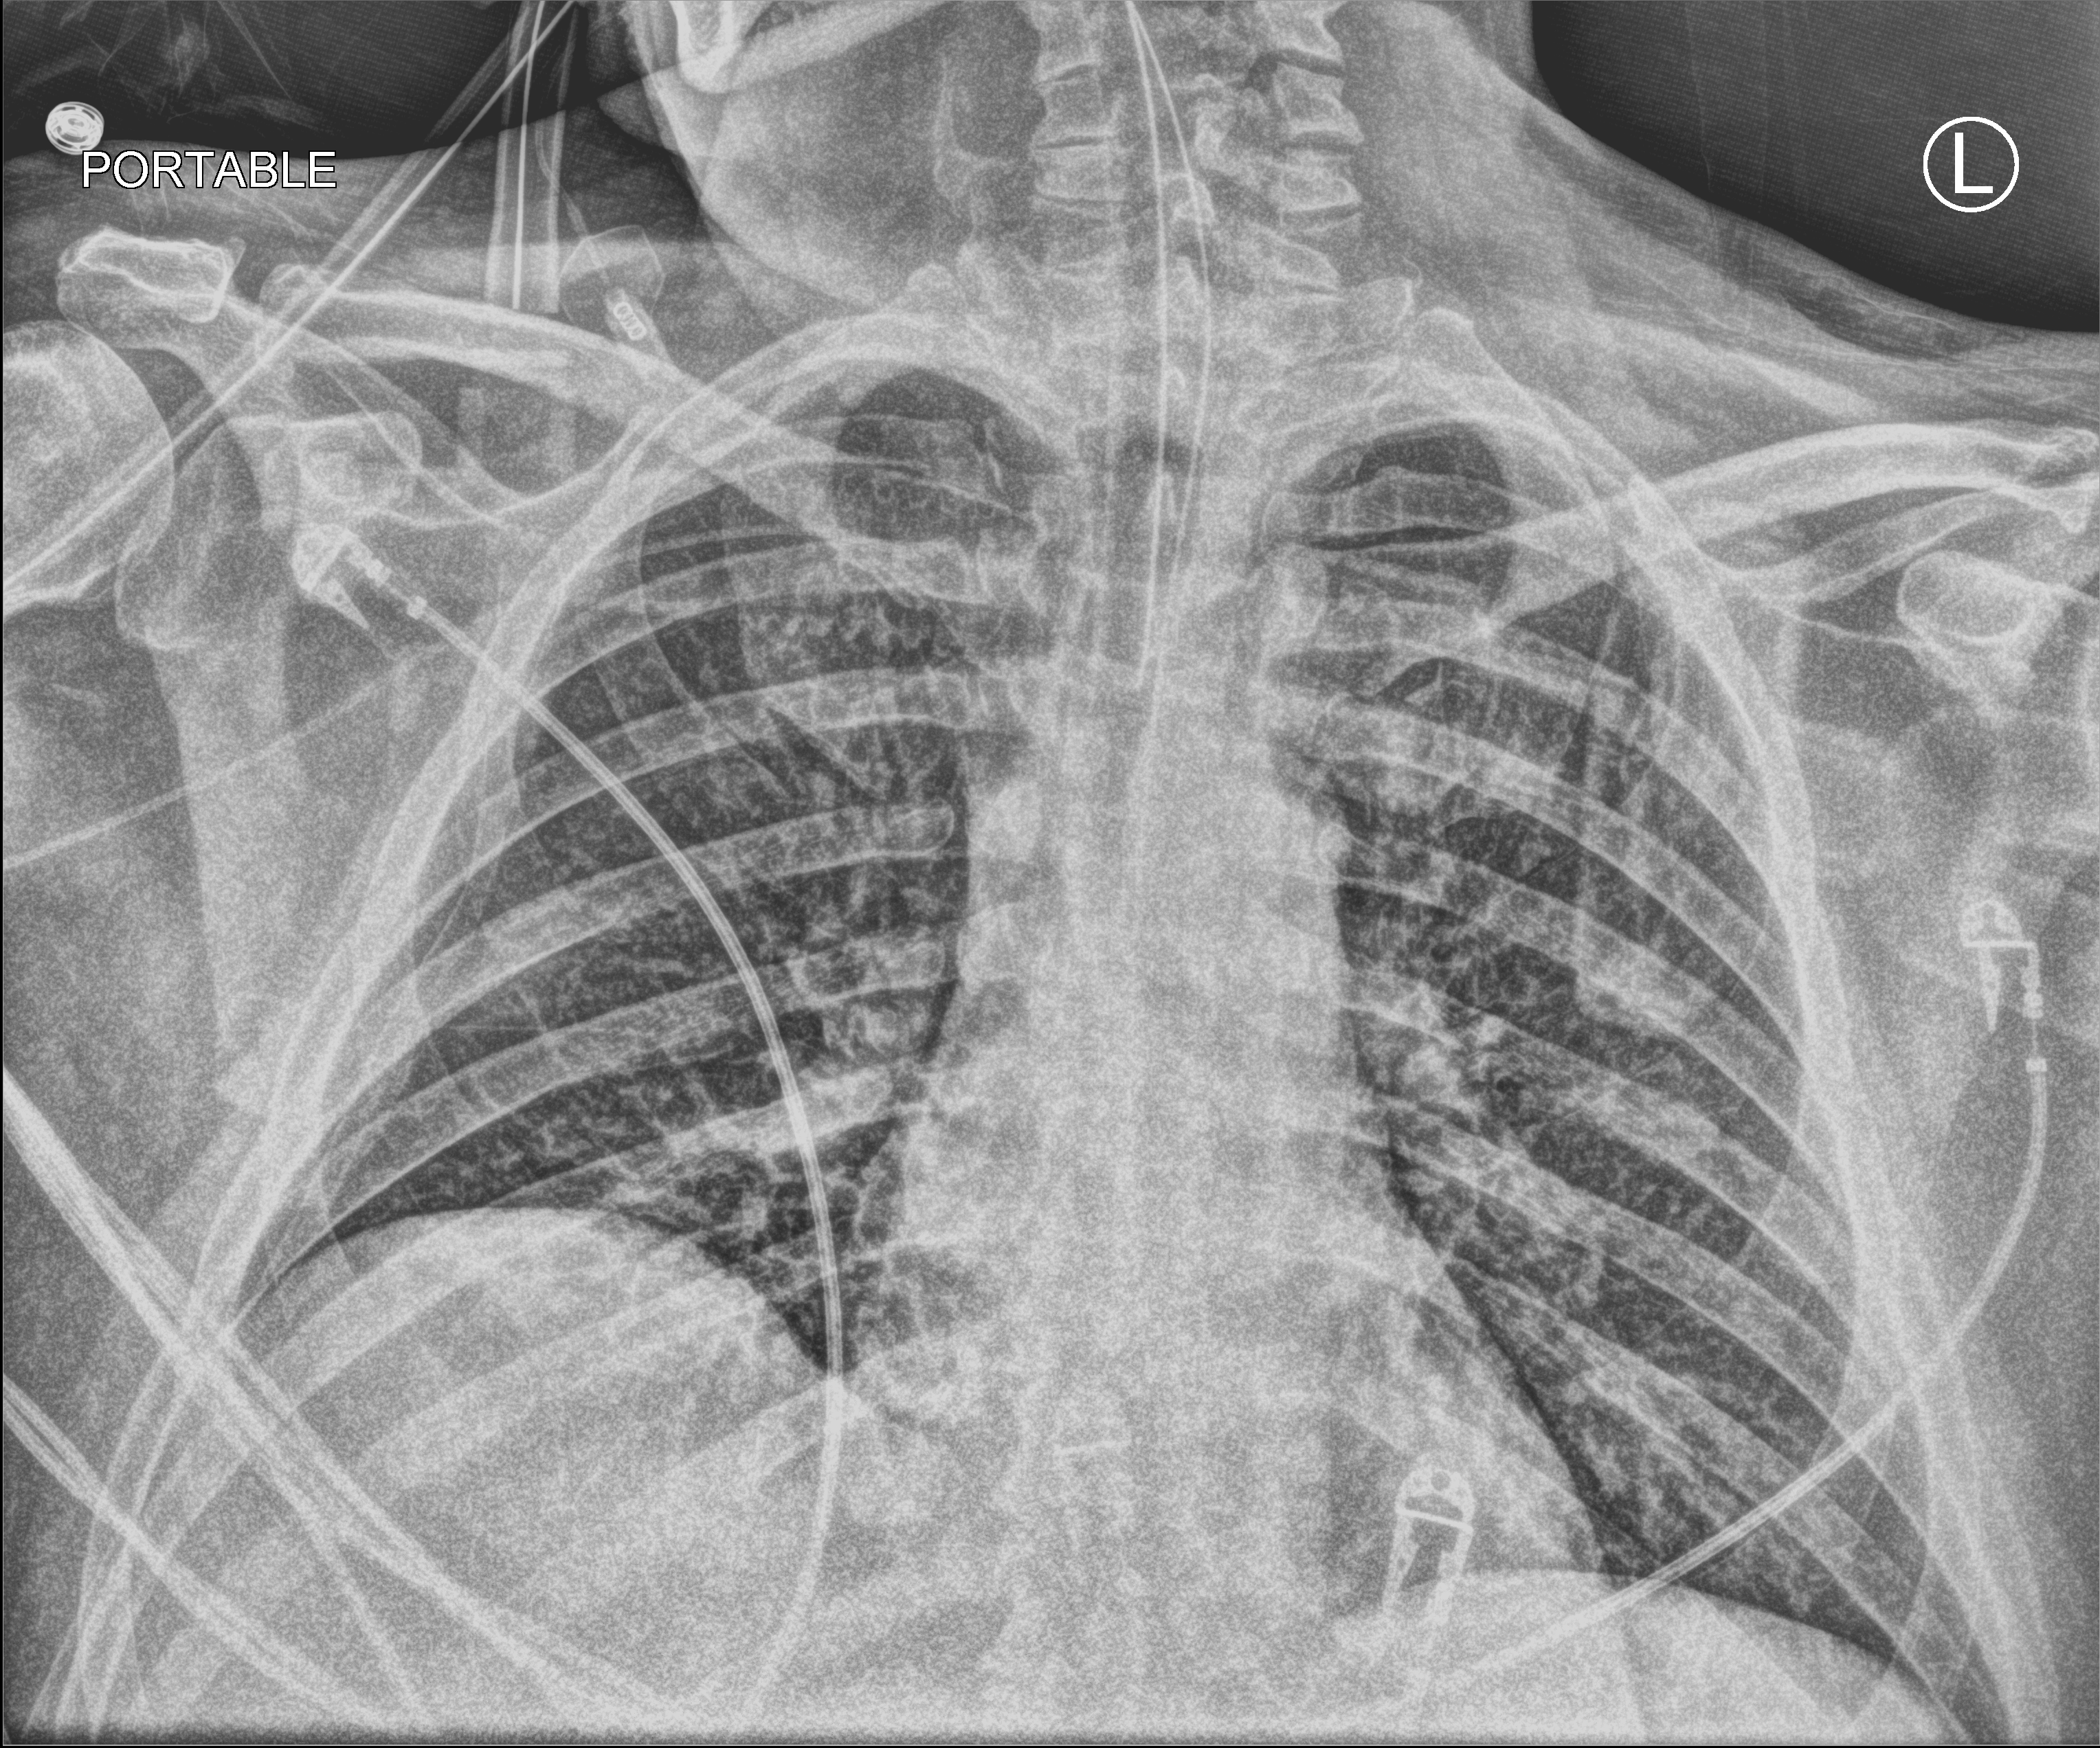
Chest X-ray (portable); anteroposterior (AP) projection. Male patient hospitalised with COVID-19, age 18–59 years.
Hospital-stay facts (about this admission, not read from this image; timing relative to this image not recorded): admitted to intensive care during this hospital stay: yes.